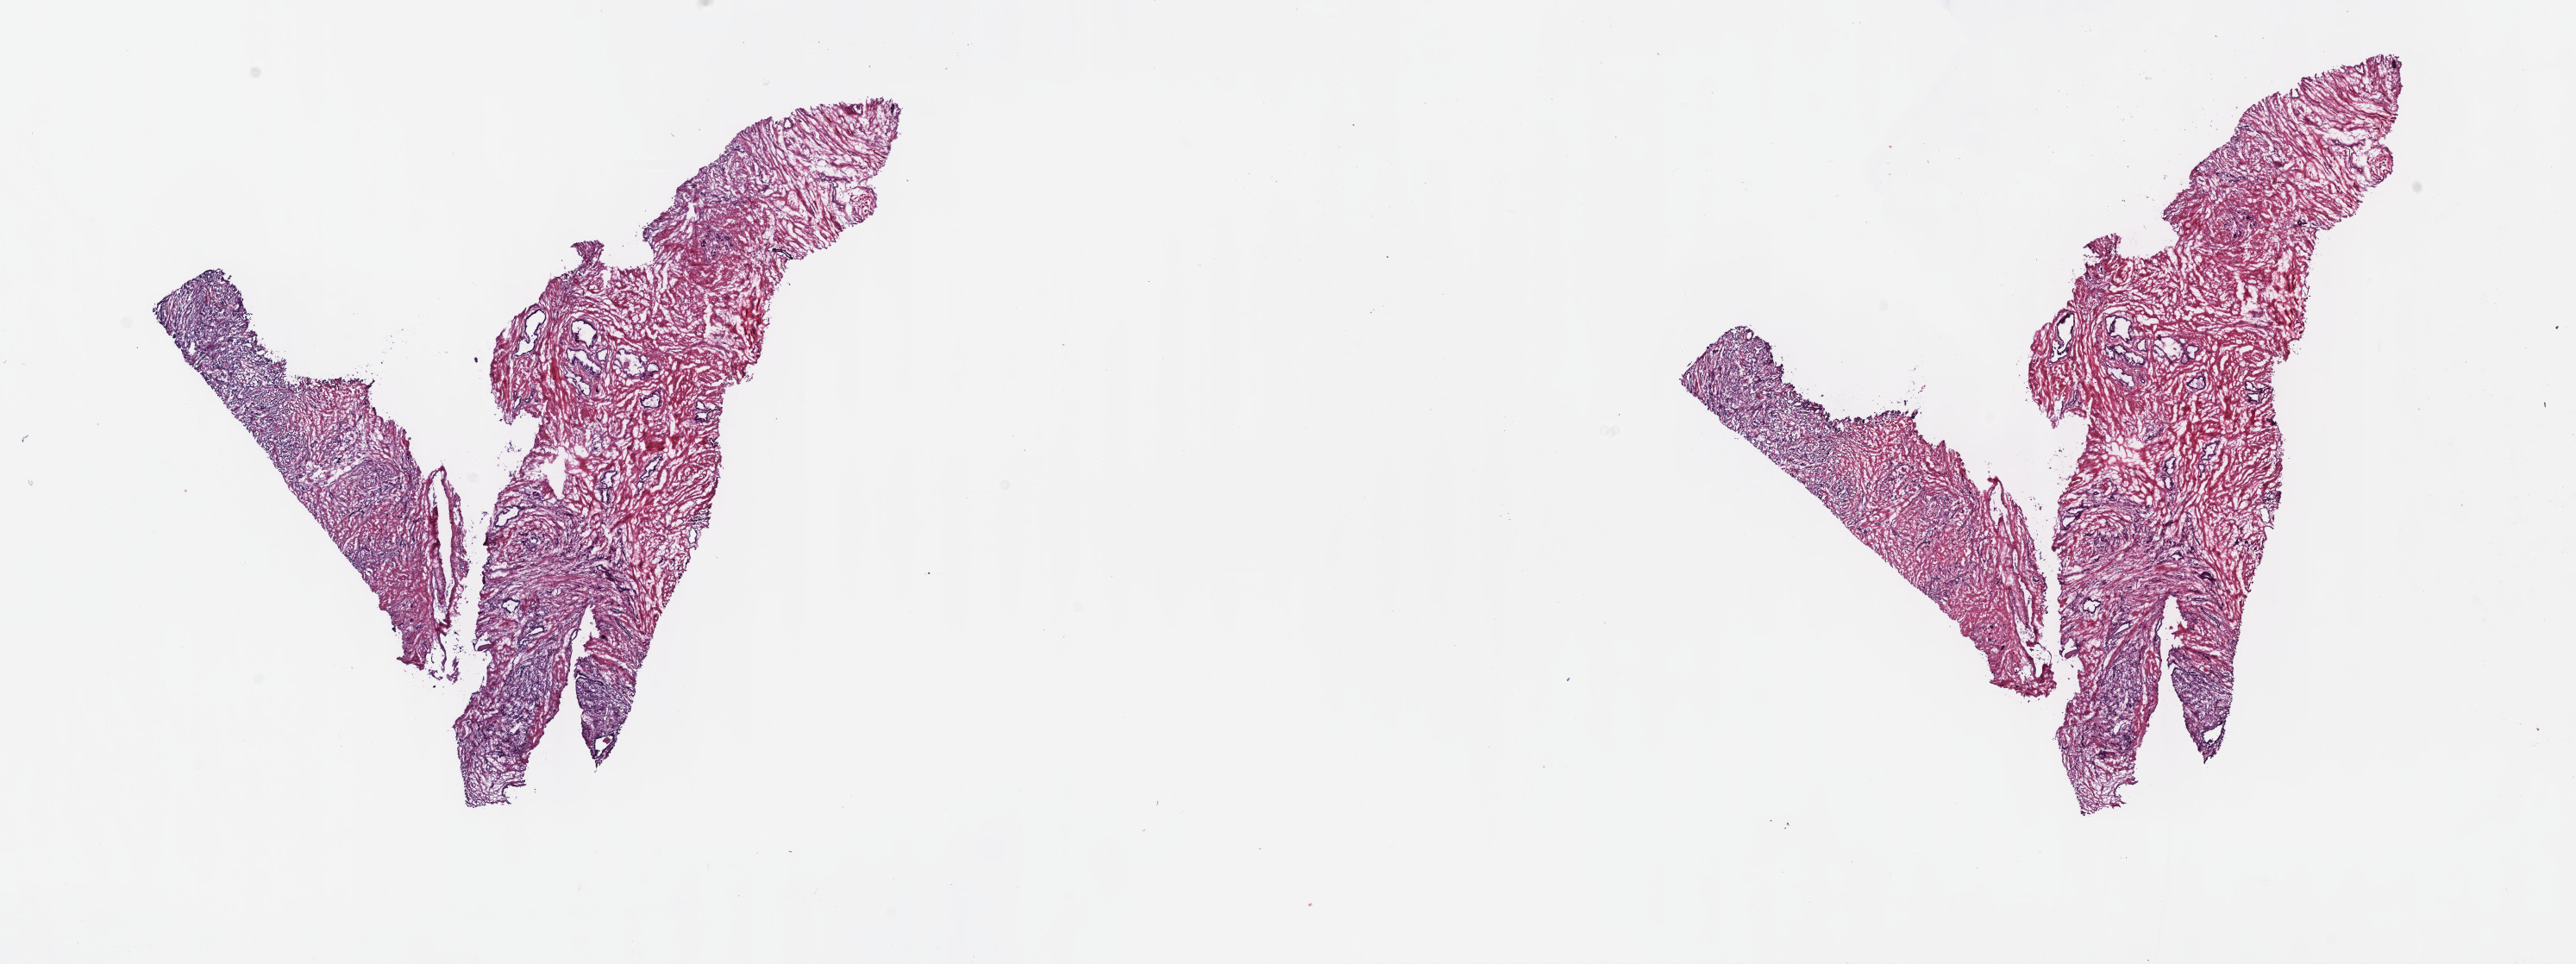
Digitized Hematoxylin and eosin (H&E) stained tissue section (whole slide), low-resolution overview of the scanned area, about 24.2 x 9.0 mm (acquisition: 40x scan), frozen section, prostate, primary tumour sample. Male, age 59 years at initial diagnosis. Gleason score: 8 (4+4). Pathologist review of this section (percent, as recorded): tumour cells 70%, tumour nuclei 70%, normal cells 0%, stromal cells 30%, necrosis 0%. Infiltration values recorded for this section: lymphocyte infiltration 60%, monocyte infiltration 5%, neutrophil infiltration 20%.
• laterality: bilateral
• histologic diagnosis: Adenocarcinoma, NOS (prostate gland)
• lymph nodes positive (case pathology): 0 of 11 examined